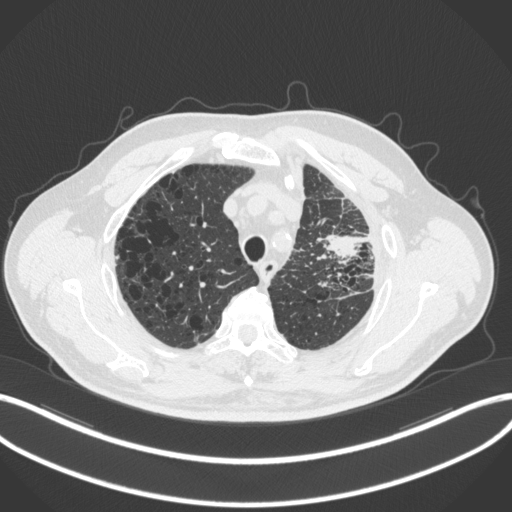
Chest CT, one axial slice; slice 247 of 286 in the series (ordered by position); 120 kVp; lung window (W 1500 / L -600 HU); 1 mm slice thickness; 512 × 512 image matrix, field of view 400 × 400 mm. Patient: male, 68 years. From the clinical record (not read from this slice): clinical TNM (as recorded): T3 N3 M1.
Annotated regions visible in this slice (bounding box drawn by a radiologist):
- lung tumour (recorded histology: adenocarcinoma): bounding box [x1, y1, x2, y2] px = [315, 228, 364, 268]